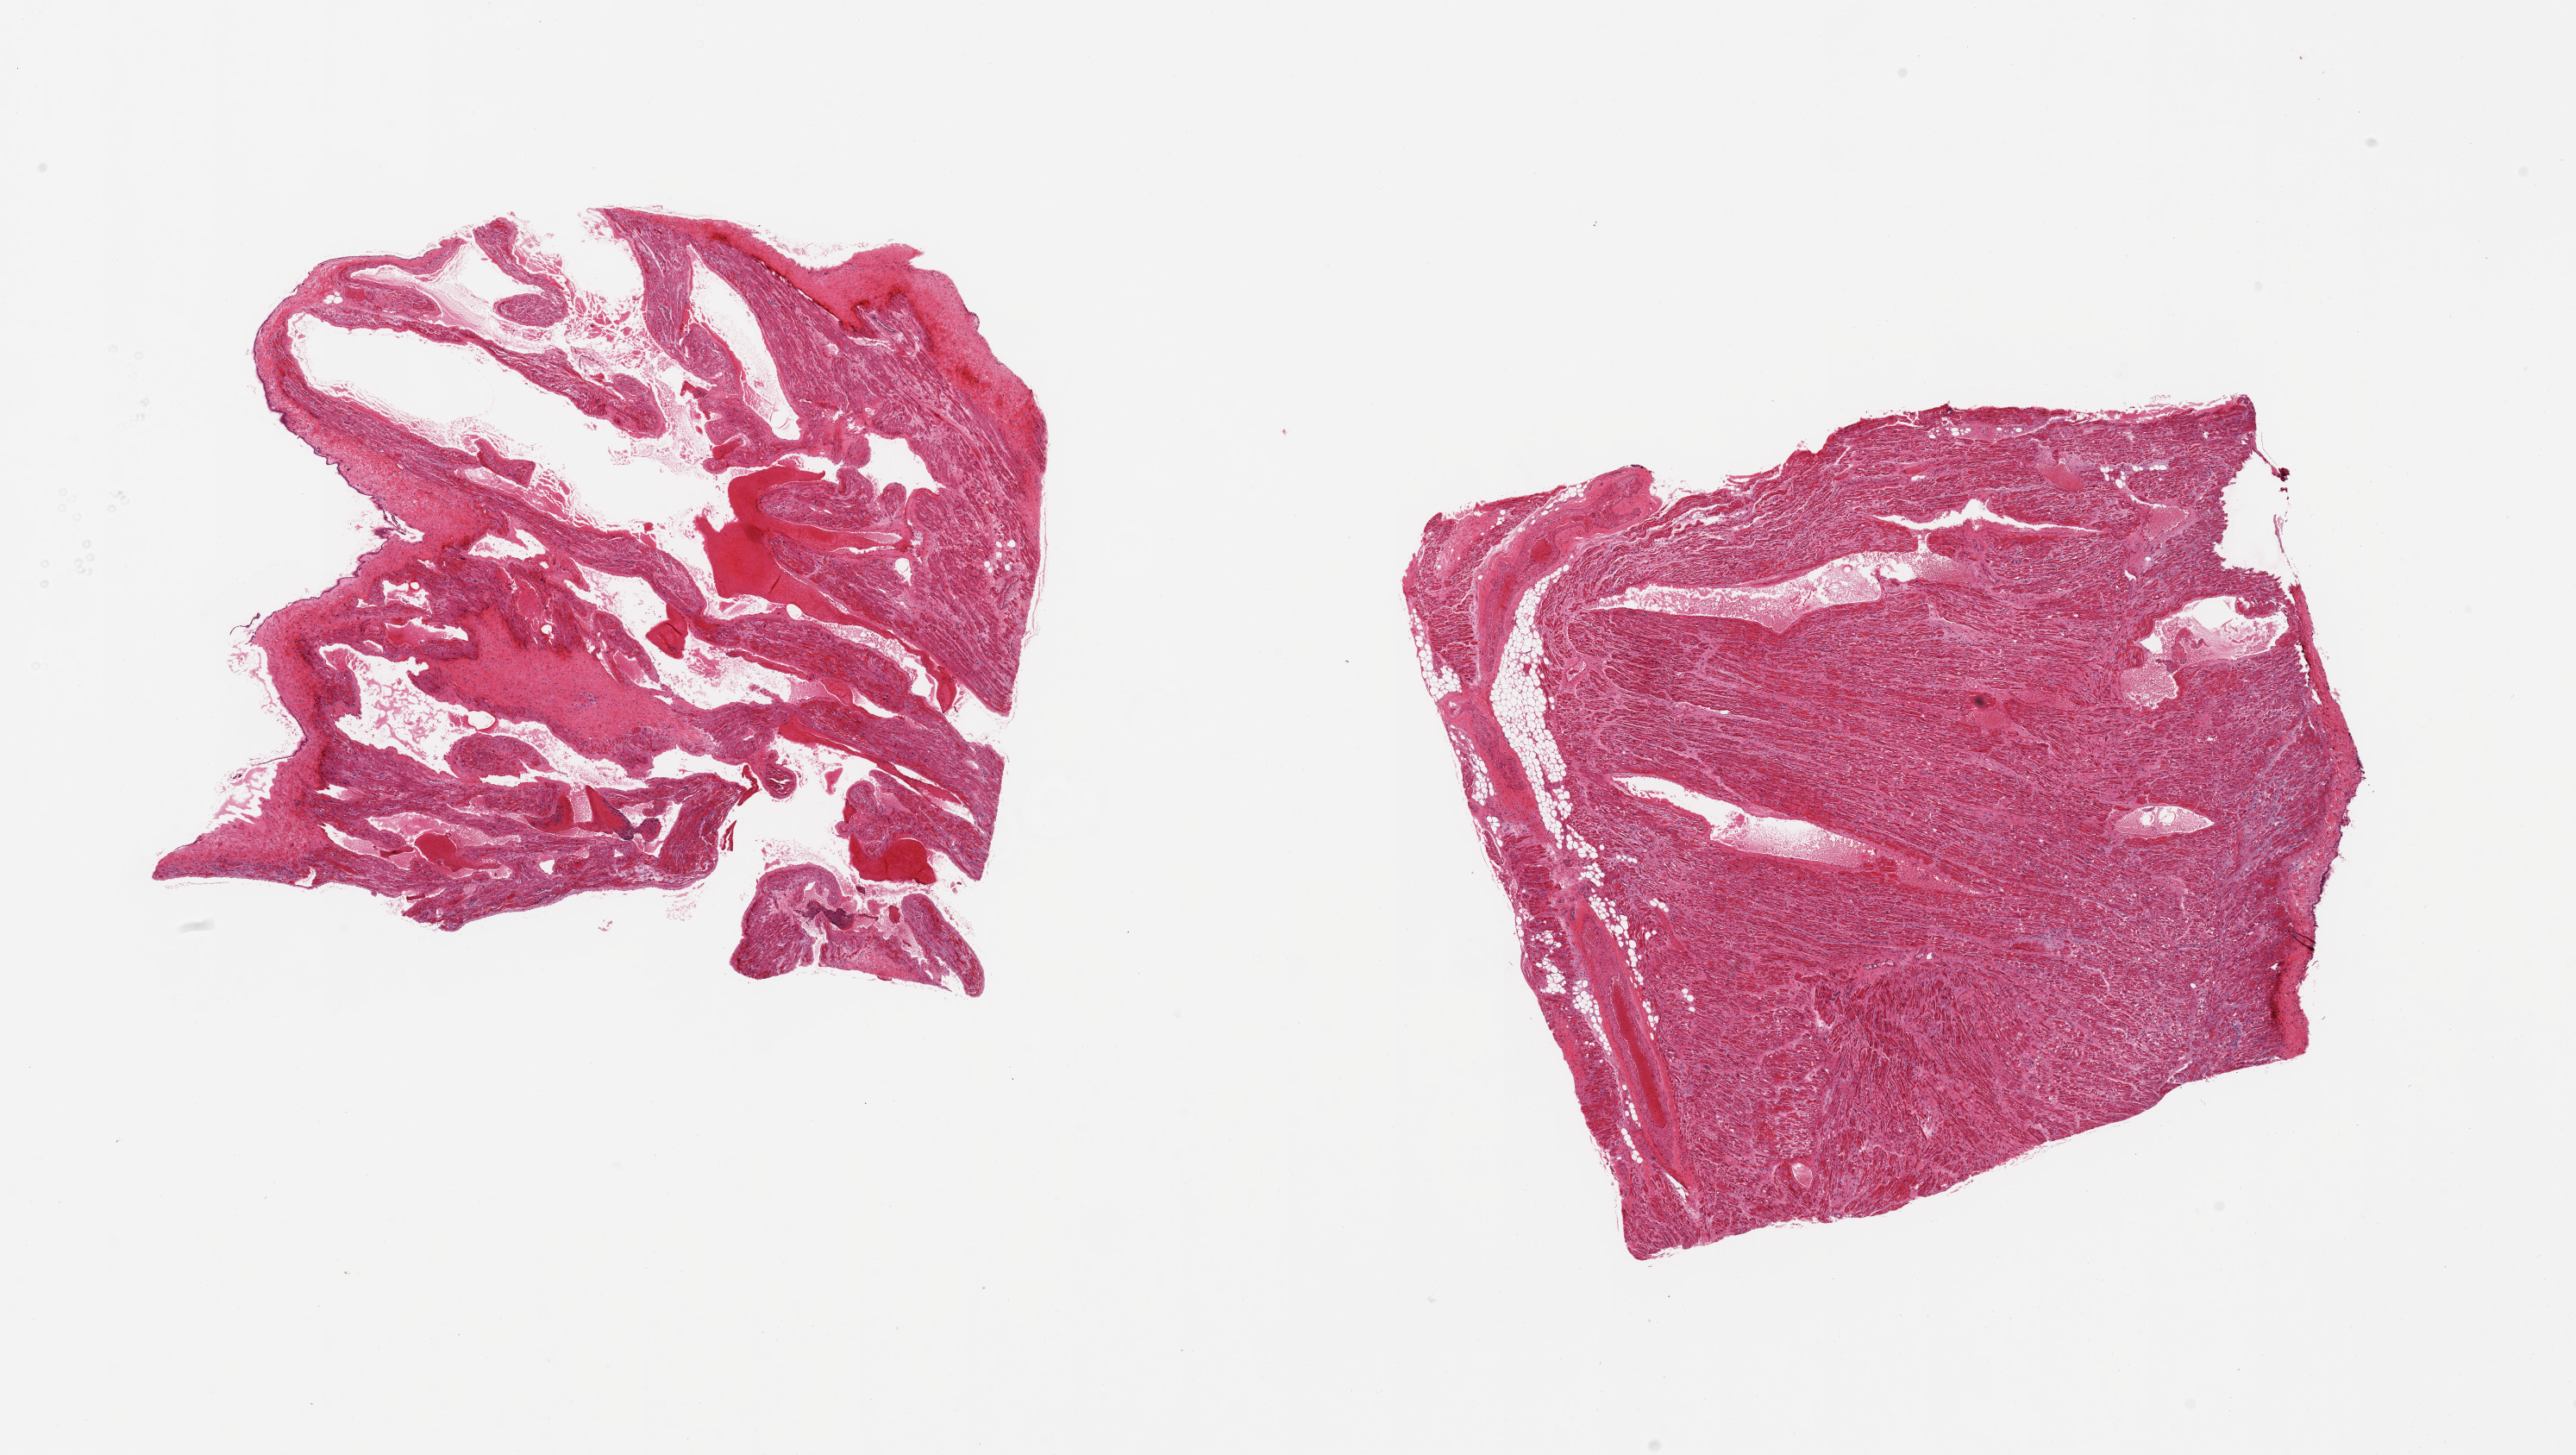
Digitized H&E-stained section, brightfield — a low-resolution overview of the entire scanned area, about 23.6 x 13.3 mm (slide scanned at 20x). PAXgene-fixed, paraffin-embedded tissue. Target tissue: auricular appendage. Tissue donor sample. Female donor.
• pathologist's review note for this sample: 2 pieces